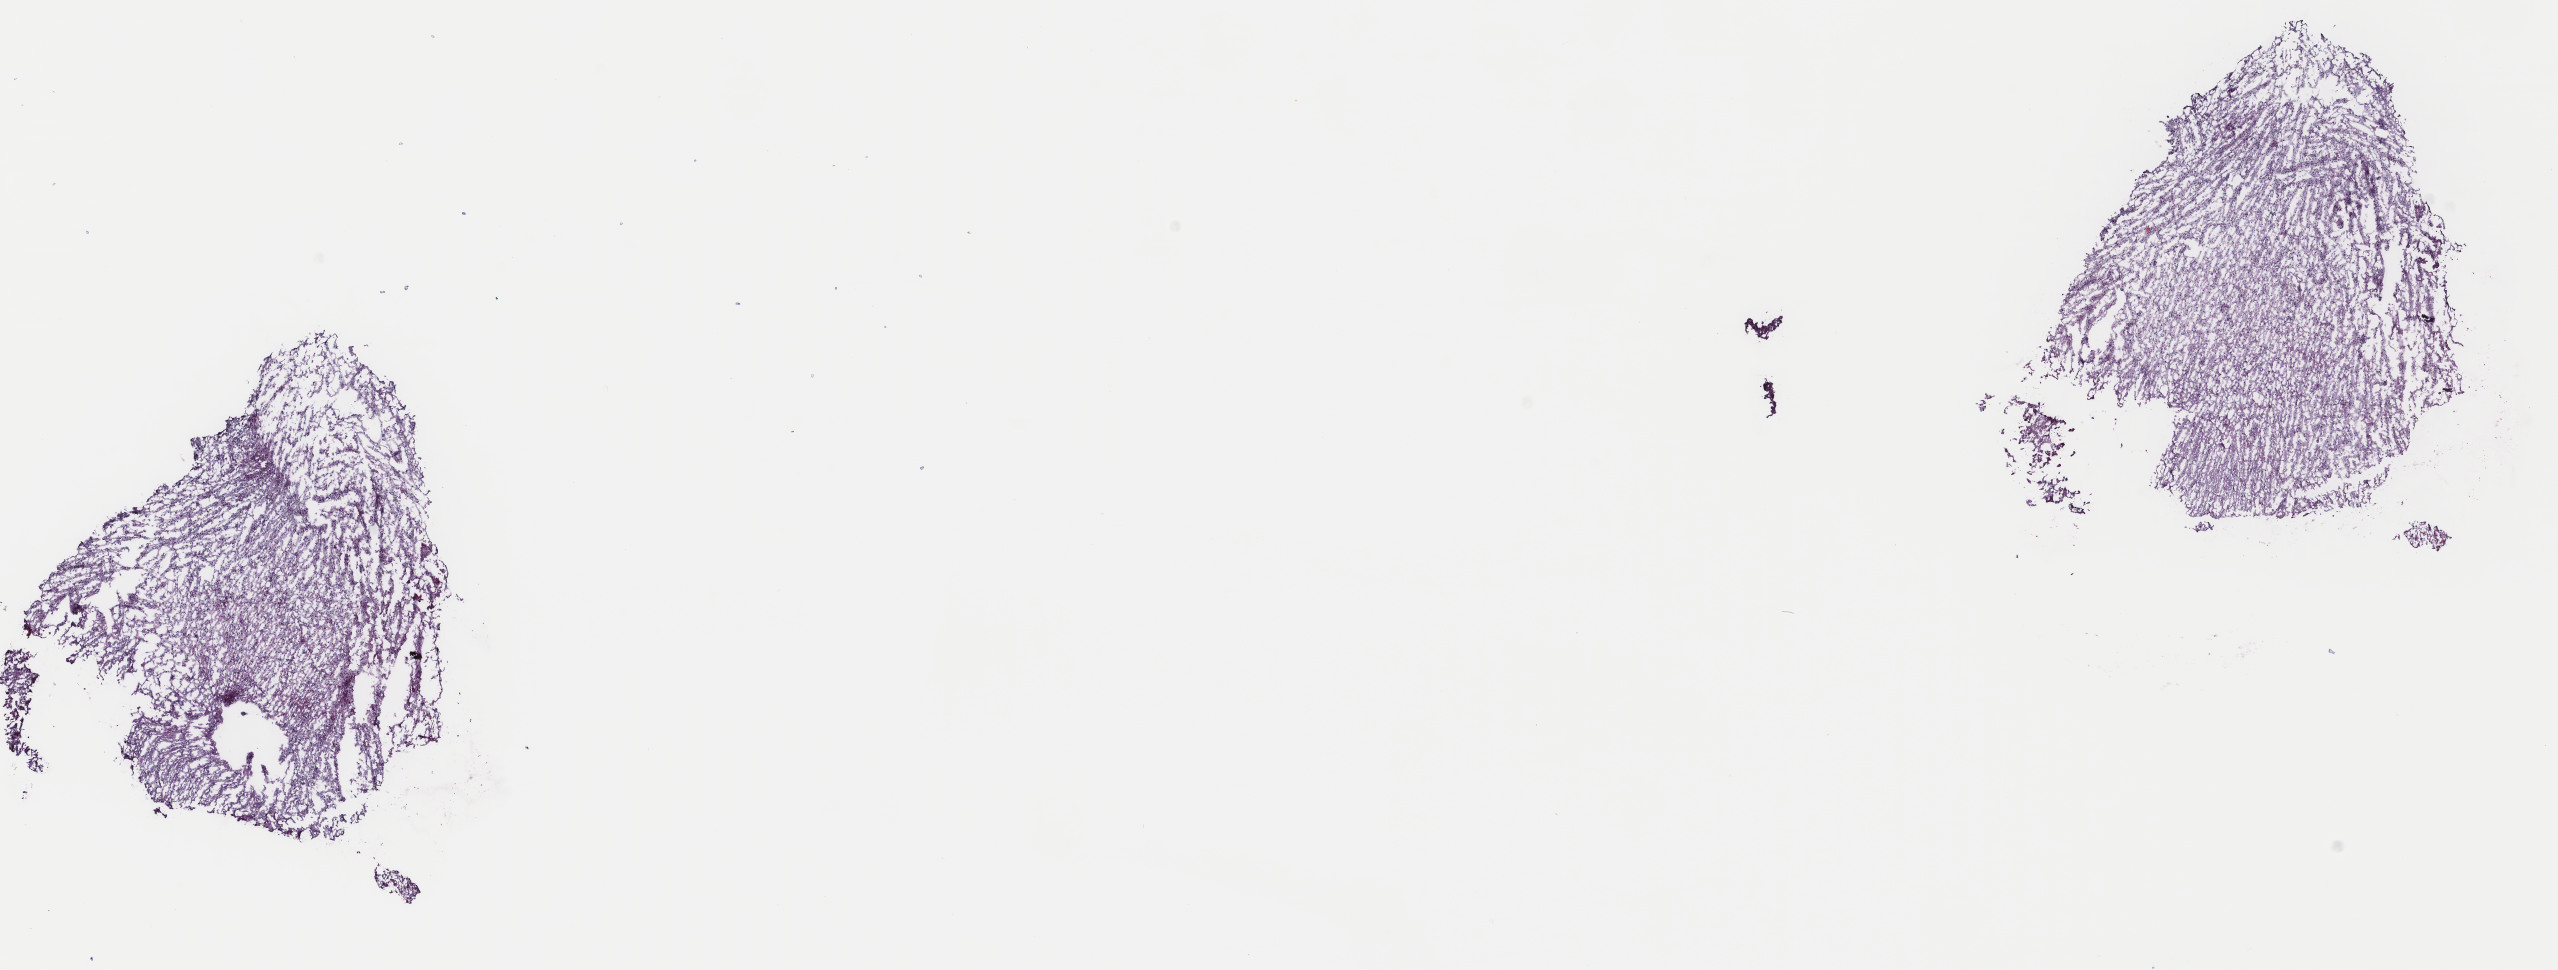
H&E-stained whole-slide image, low-resolution overview of the scanned area, about 20.3 x 7.7 mm (acquisition: 40x scan); frozen section from the top of the tissue portion; brain, primary tumour sample. Female patient; age at initial diagnosis 72 years. Pathologist review of this section (percent, as recorded): tumour cells 40%, tumour nuclei 80%, normal cells 10%, stromal cells 50%, necrosis 0%. Infiltration values recorded for this section: lymphocyte infiltration 0%, monocyte infiltration 0%, neutrophil infiltration 0%.
Histologic diagnosis: Glioblastoma (frontal lobe).